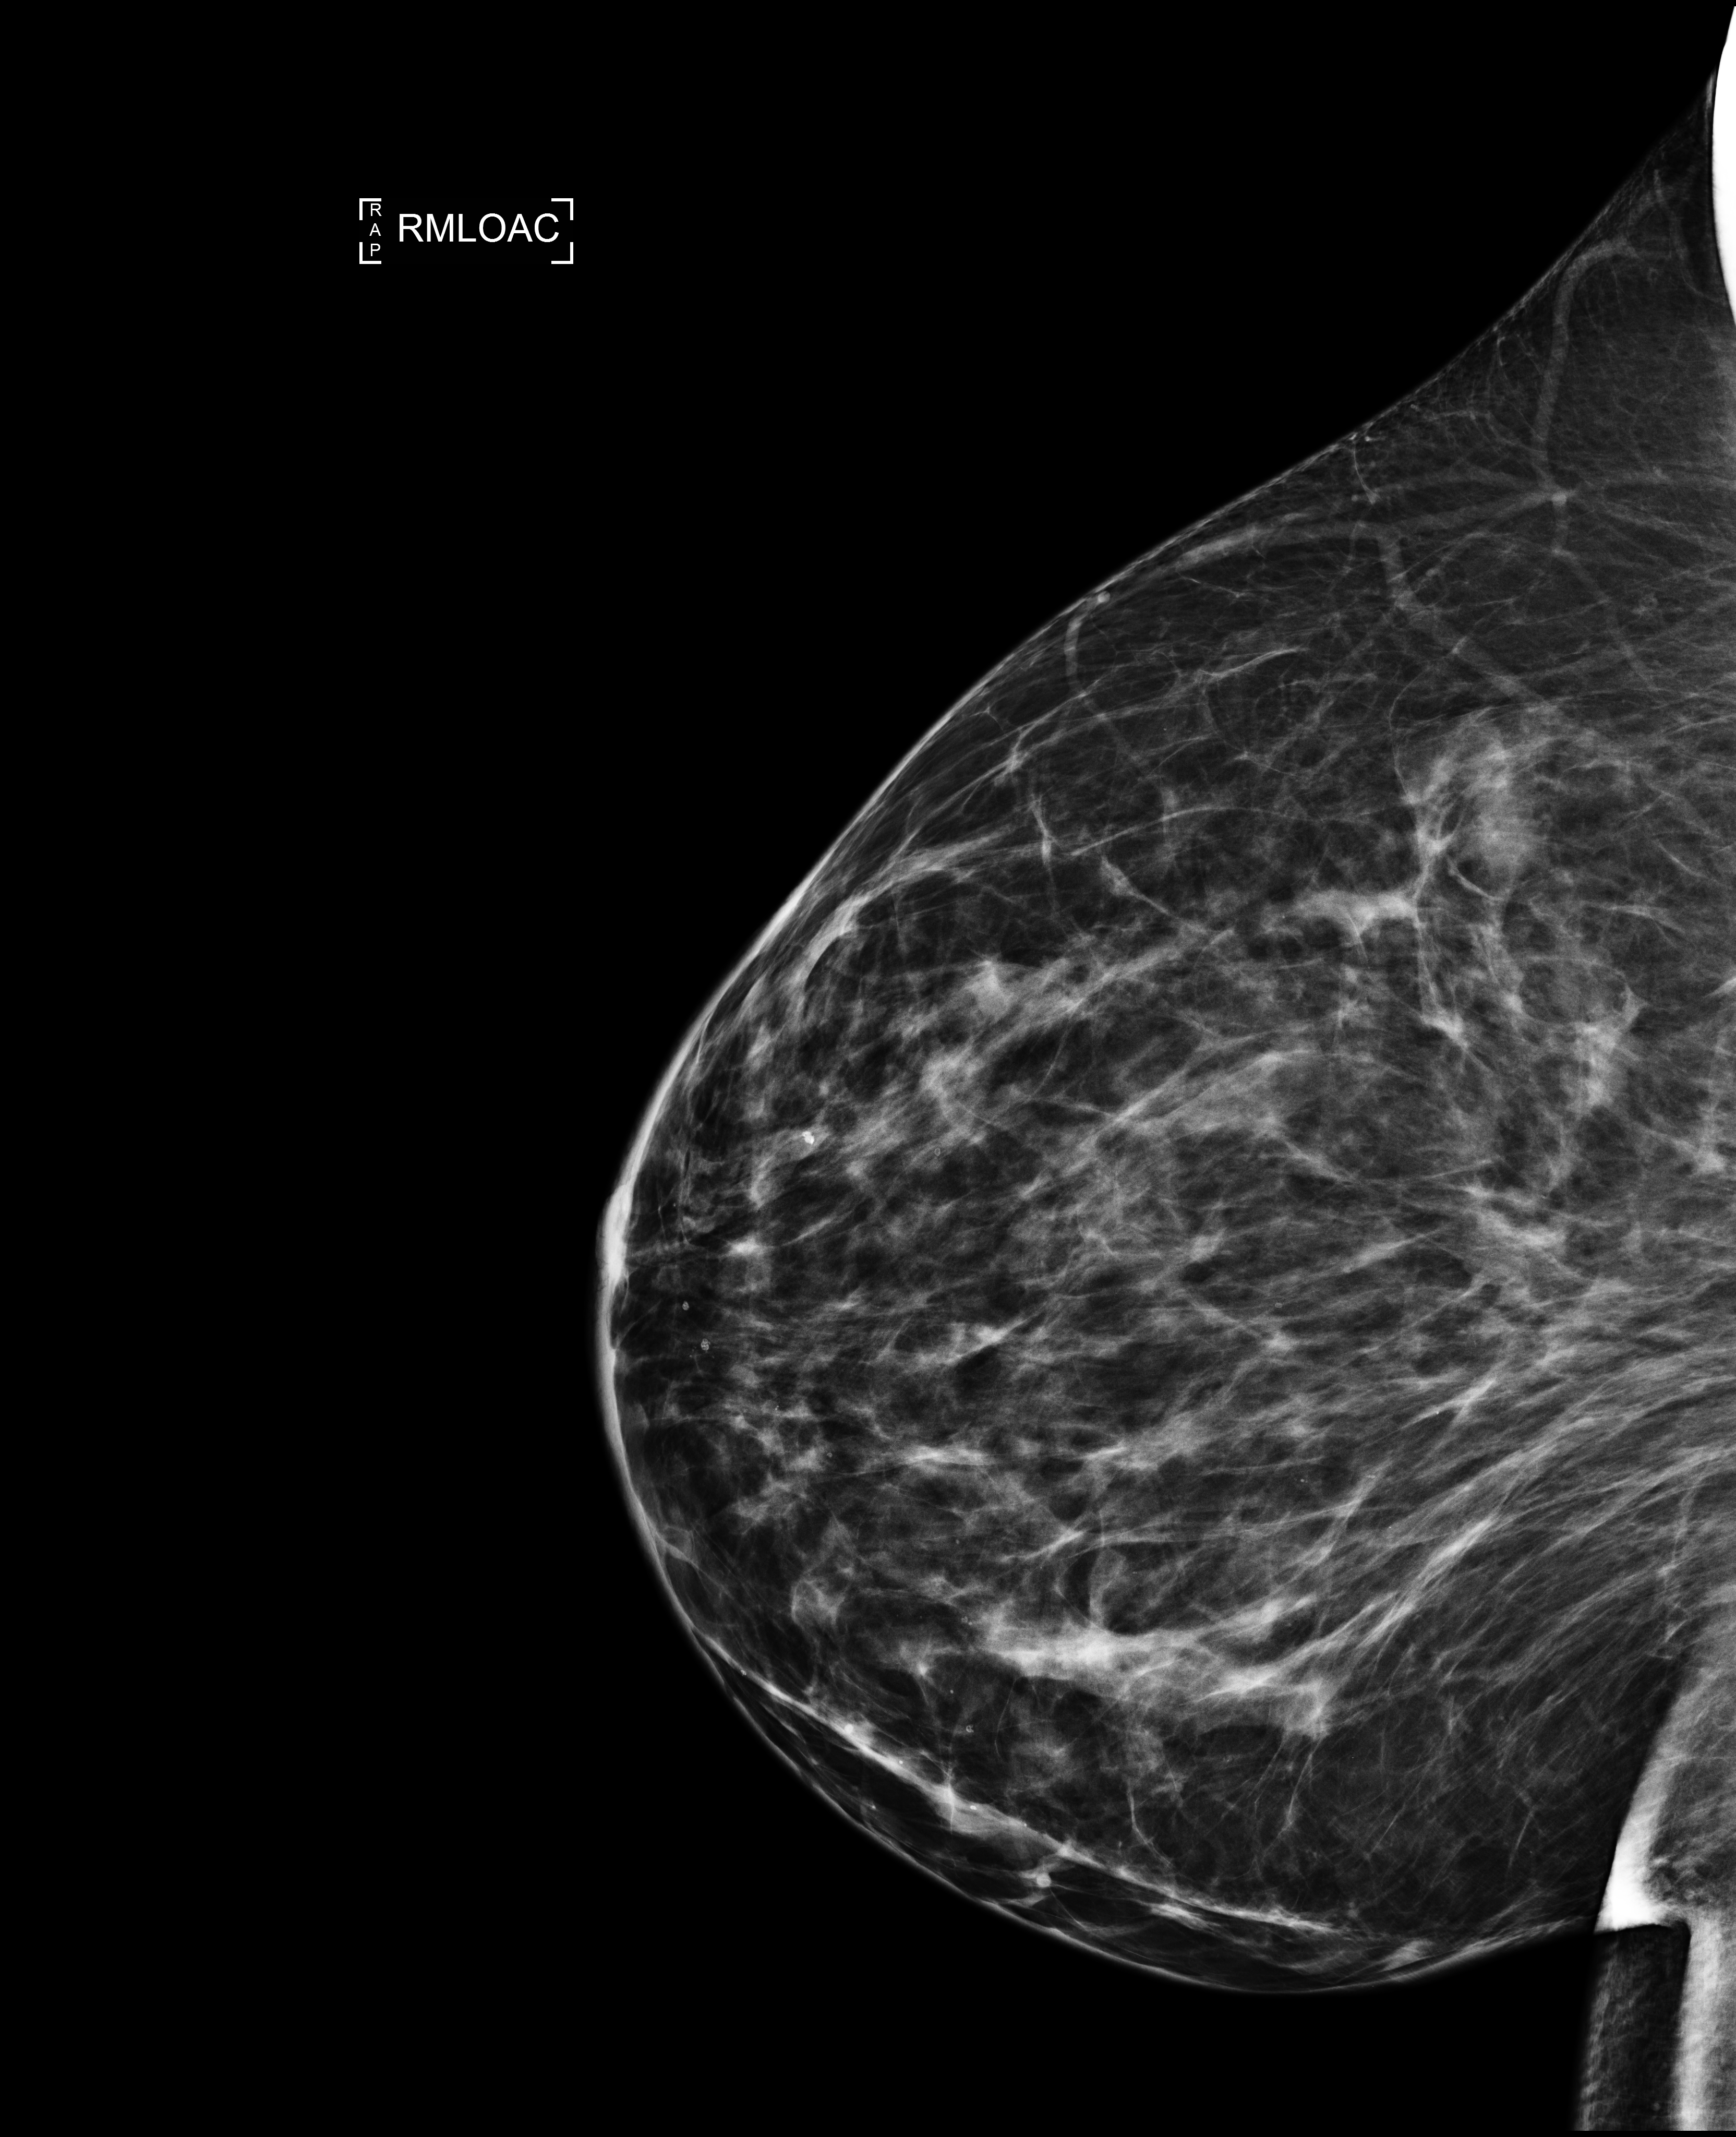
Screening examination, system: Selenia Dimensions. Patient: female, 46 years.
Image type: full-field digital mammogram. Breast: right. Projection: mediolateral oblique (MLO) view, anterior compression.